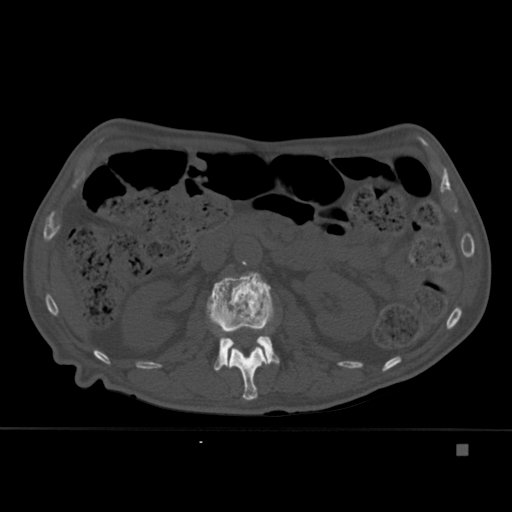
CT including the spine, one axial slice. Slice 172 of 451 in the series (ordered by position). Bone window (W 1800 / L 400 HU). 1.5 mm slice thickness. 512 × 512 image matrix, field of view 378 × 378 mm. Male patient, age 75 years. Case-level facts recorded for this patient, not image findings: primary cancer: prostate.
Annotated regions visible in this slice (semi-automatic segmentation, software-assisted and operator-edited):
- L1 vertebra: bounding box [x1, y1, x2, y2] px = [224, 332, 270, 400]
- L2 vertebra: [206, 272, 280, 372]